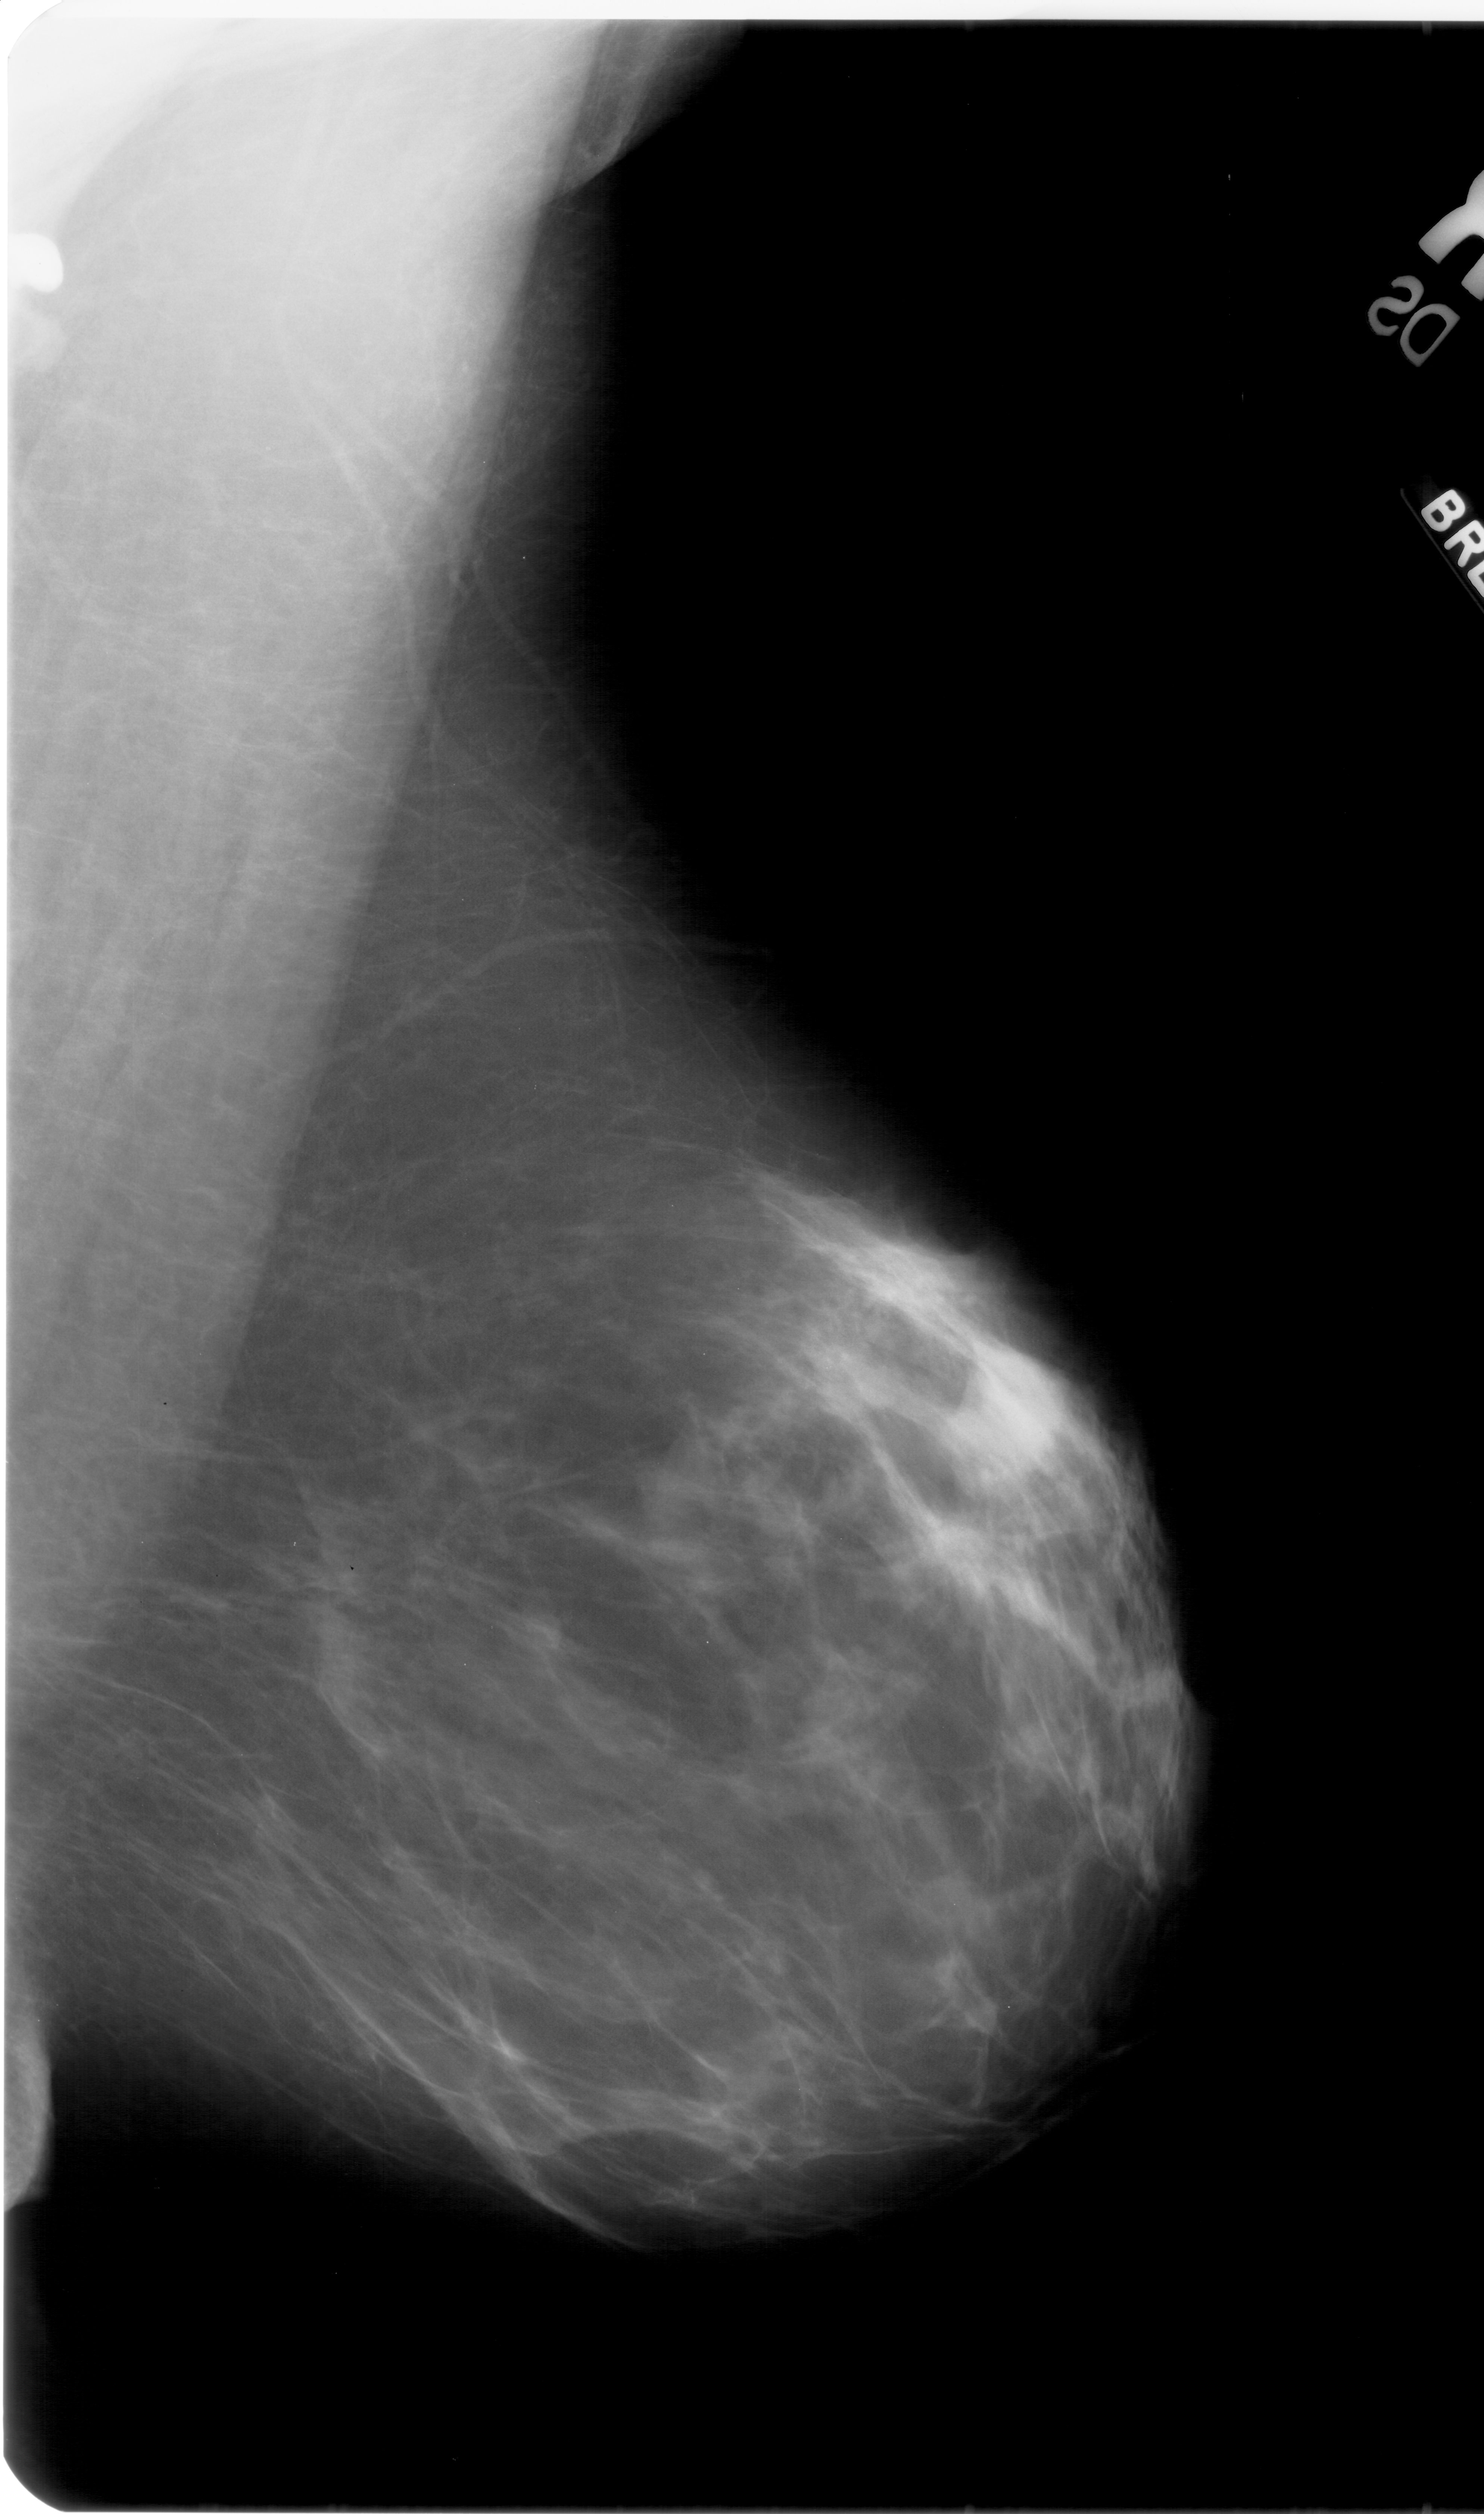
Scanned film-screen mammogram; right breast; mediolateral oblique (MLO) view; 1484 × 2514 image matrix.
Expert-marked regions of interest on this image (one box per marked abnormality):
- mass, shape lobulated, margins ill defined; BI-RADS assessment category 4; pathology result (as recorded, not read from the image): benign: bounding box <964,1342,1073,1459> (left, top, right, bottom; pixels)